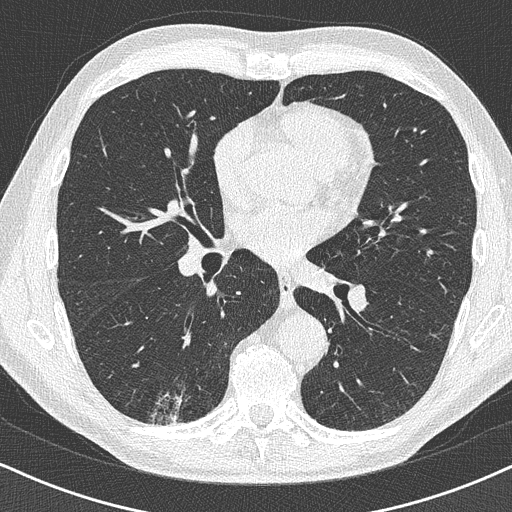
Low-dose screening chest CT, axial slice, baseline annual screen, lung window (W 1500 / L -600 HU), slice 218 of 438 in the series. Male, age 63 years at enrolment. Former smoker at enrolment.
Expert-annotated lung lesion, bounding box <132,364,204,428> (left, top, right, bottom; pixels). The exam's reader record, not a measurement of the box and not confirmed to be the same lesion: non-calcified nodule or mass ≥4 mm, right lower lobe, 16 × 13 mm, poorly defined margins. Participant outcome: lung cancer diagnosed 74 days after this screen — adenocarcinoma, NOS, right lower lobe, moderately differentiated (G2), stage IA (AJCC 6th edition), 20 mm at pathology.